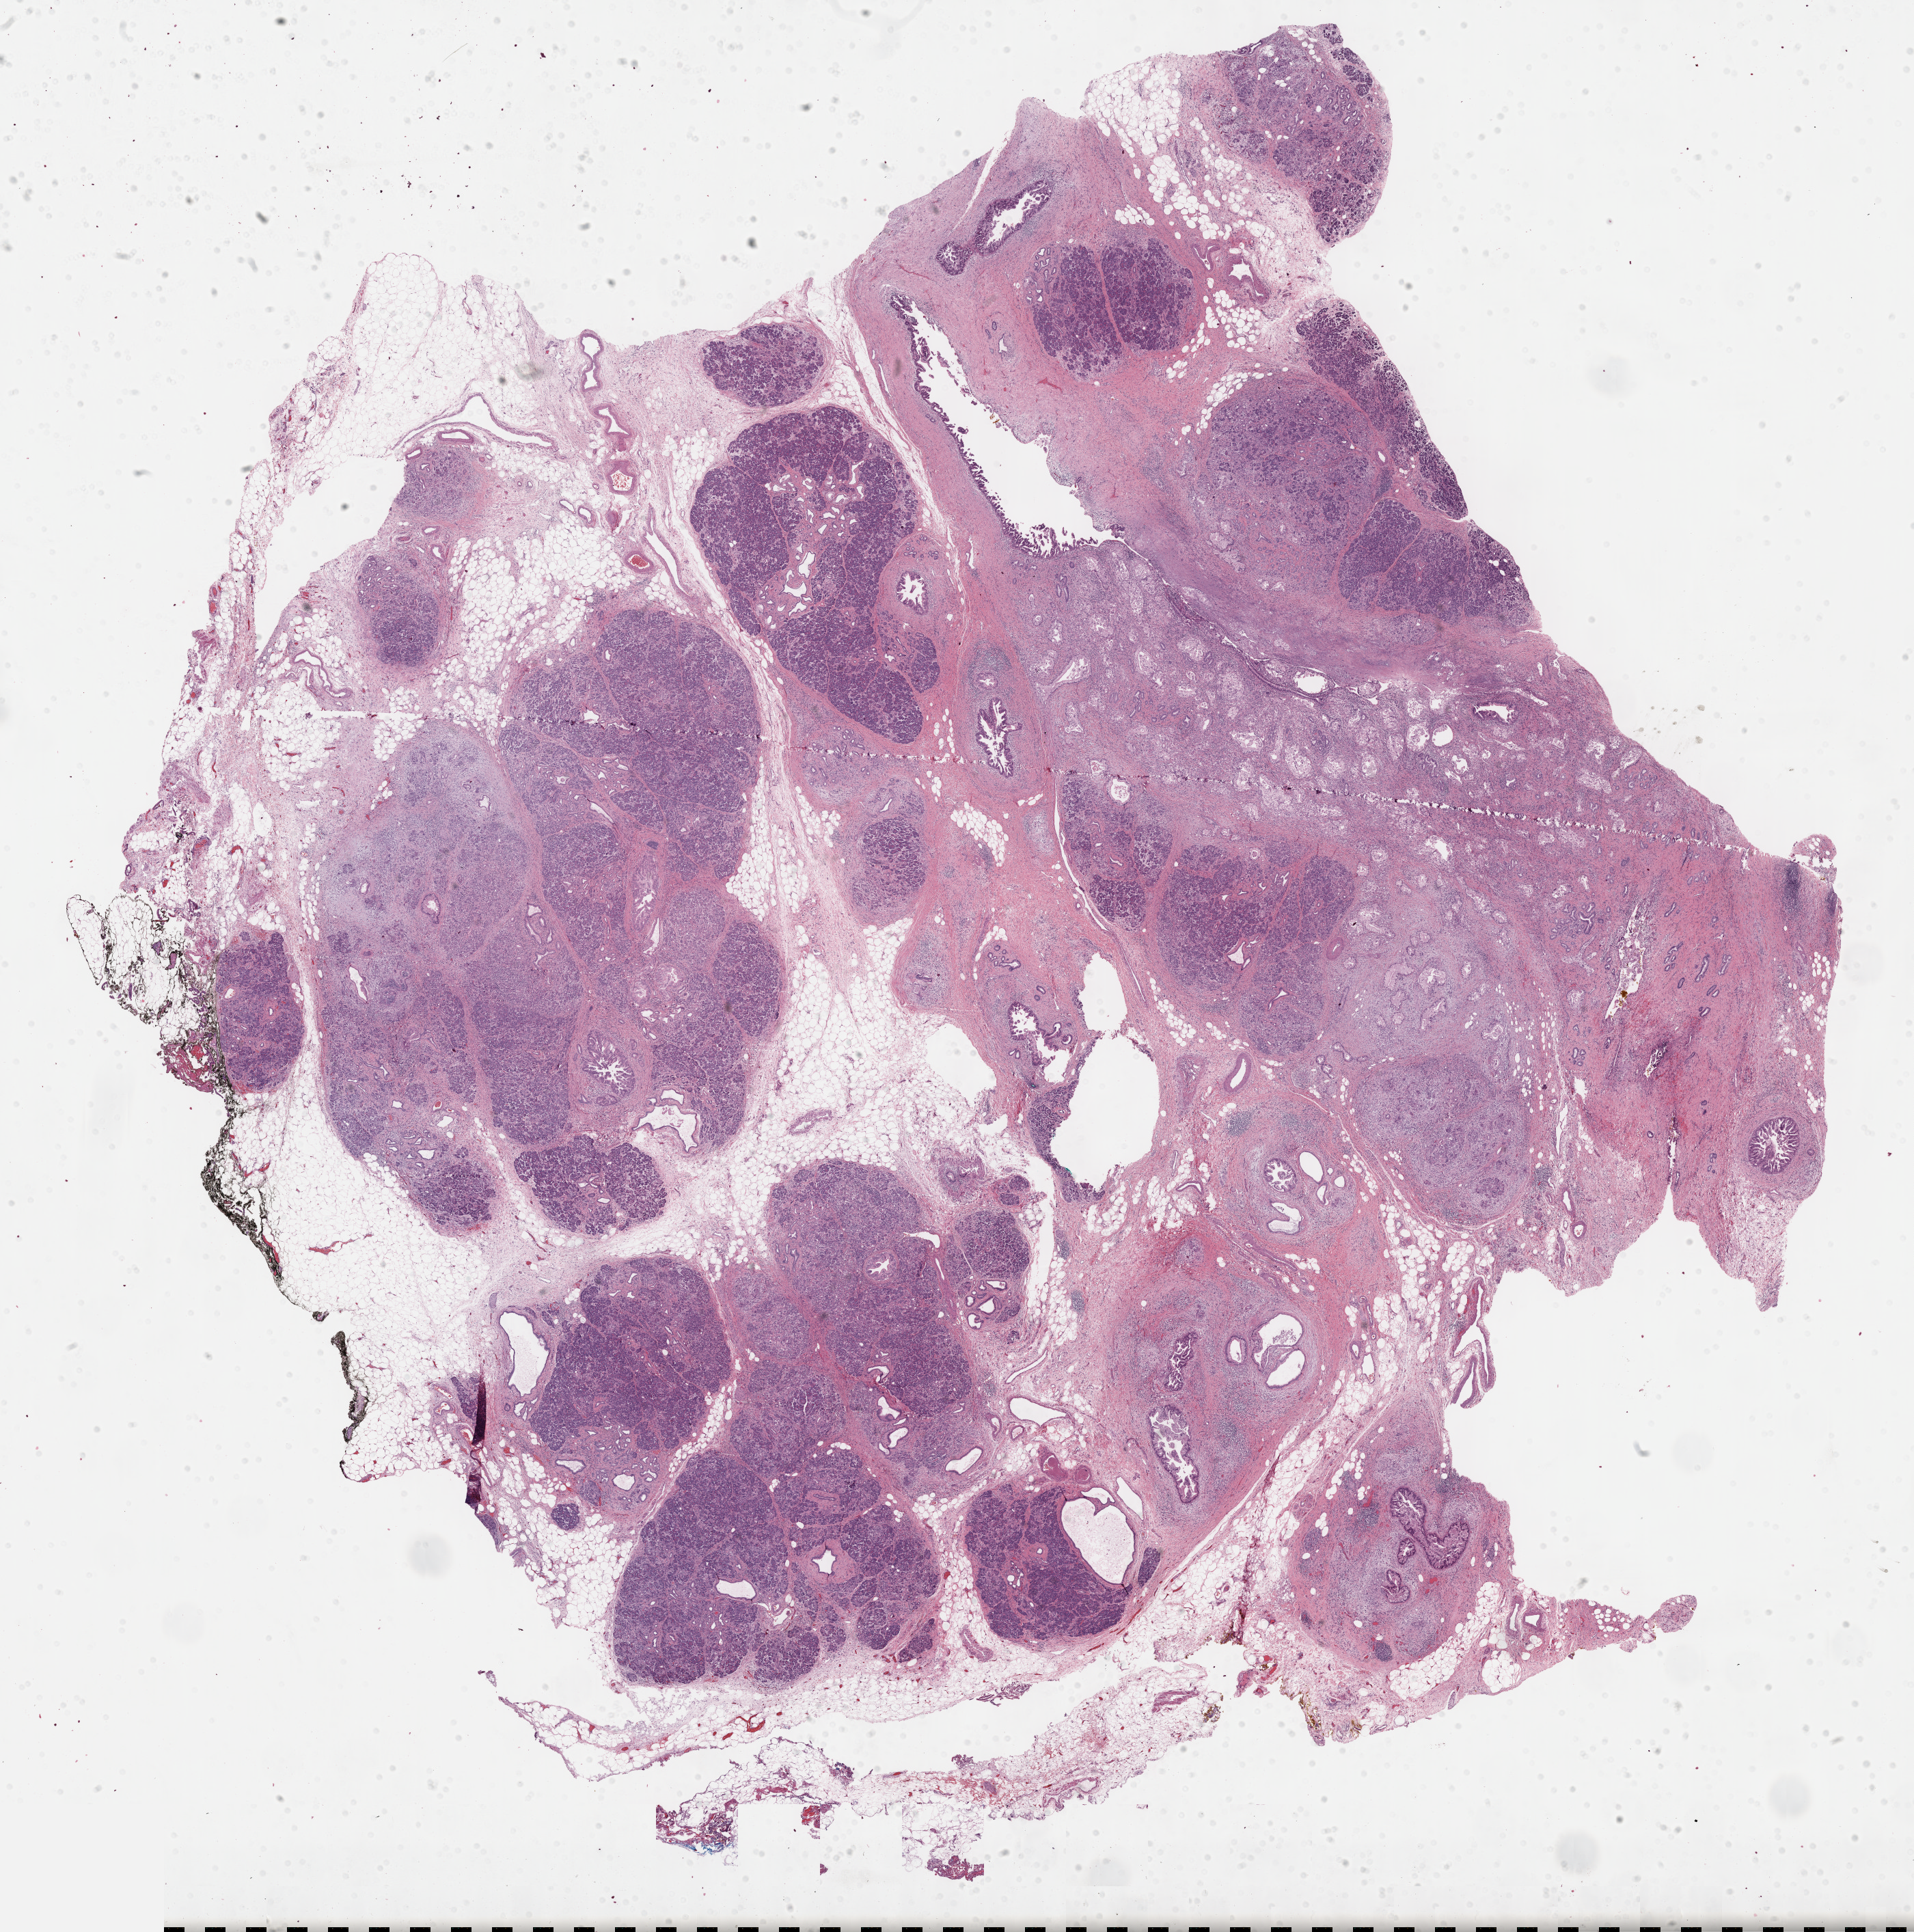
Hematoxylin and eosin (H&E) stained whole-slide image — low-resolution overview of the scanned area, about 22.7 x 22.9 mm (from a 40x scan); formalin-fixed paraffin-embedded (FFPE) diagnostic section; primary tumour sample from the pancreas. Female, age 85 years at initial diagnosis. Histologic grade: GX (grade cannot be assessed).
- pathologic diagnosis: Infiltrating duct carcinoma, NOS (head of pancreas)
- lymph nodes positive (case pathology): 1 of 10 examined
- AJCC pathologic stage: IIB
- TNM: T3 N1 M0